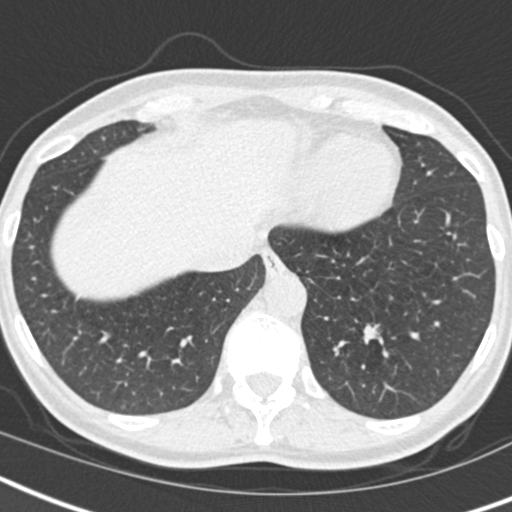
Low-dose screening chest CT, one axial slice. Position 48 of 173 along the scan axis. Reconstruction kernel B30f. Lung window (W 1500 / L -600 HU). 512 × 512 image matrix, field of view 293 × 293 mm.
Annotated regions visible in this slice (expert manual segmentation):
- lesion 1 (tumor, lower lobe of left lung): bounding box (x1, y1, x2, y2) in pixels: (363, 323, 382, 344)